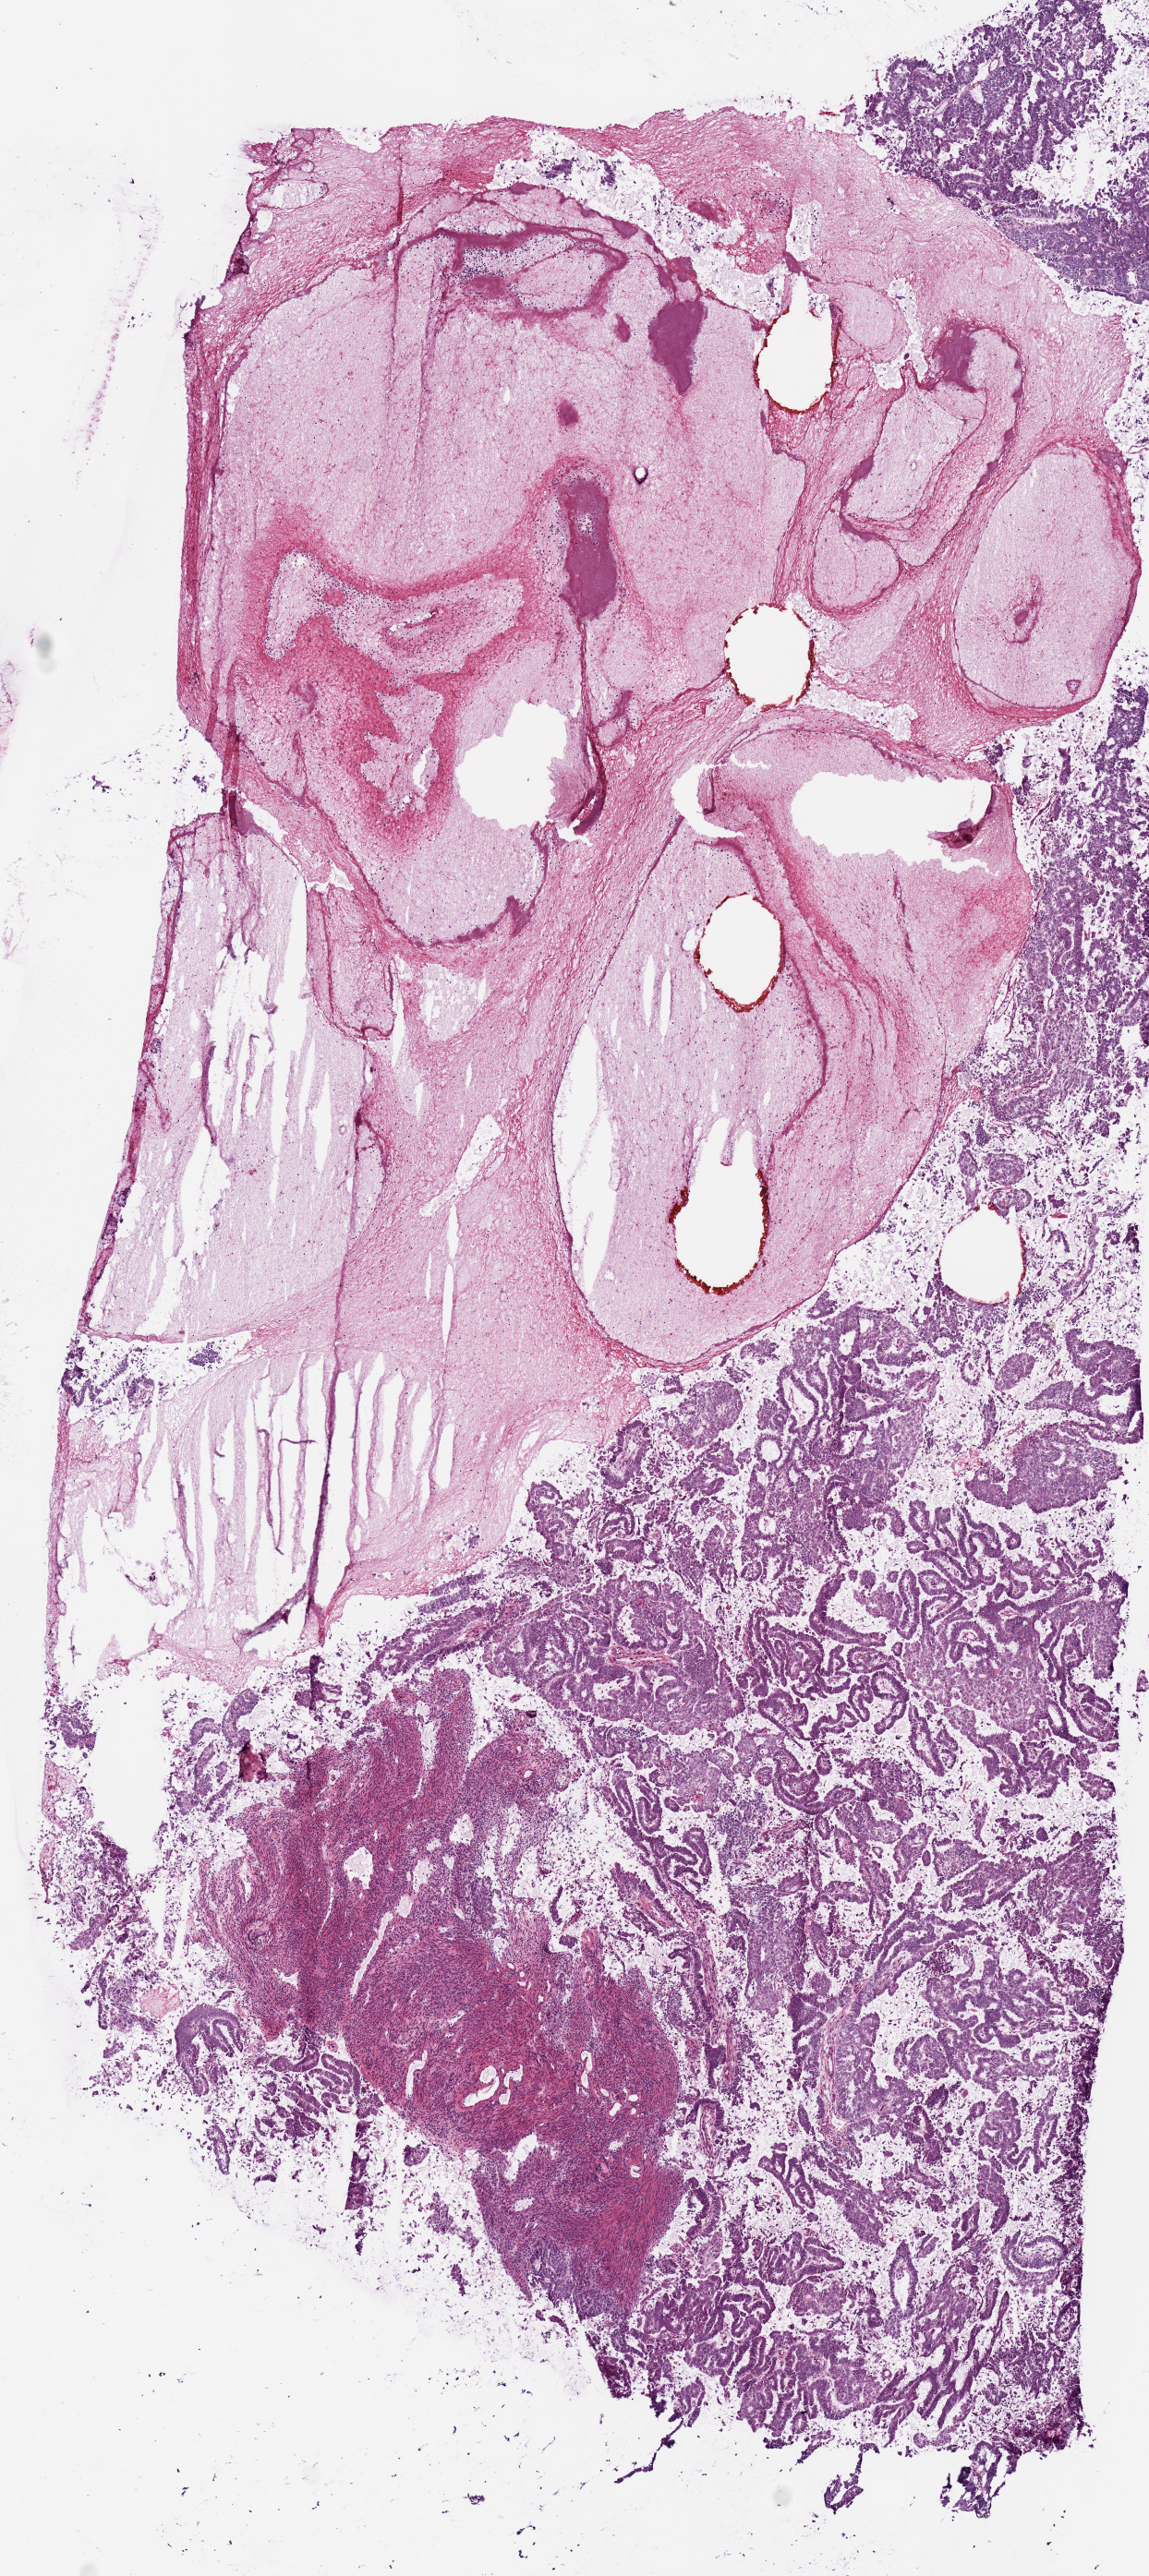
Whole-slide histology image, H&E-stained, a low-resolution overview of the entire scanned area, about 4.9 x 11.0 mm (slide scanned at 20x), frozen section from the top of the tissue portion, primary tumour sample from the uterus. Patient: female, age at initial diagnosis 56 years. Histologic grade: G3 (poorly differentiated). Pathologist review of this section (percent, as recorded): tumour cells 90%, tumour nuclei 75%, normal cells 0%, stromal cells 10%, necrosis 0%. Infiltration values recorded for this section: lymphocyte infiltration 0%, monocyte infiltration 0%, neutrophil infiltration 0%.
• diagnosis: Serous cystadenocarcinoma, NOS
• FIGO stage: IB